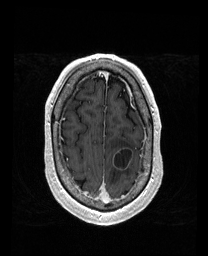
Brain MRI from a brain-tumour surgery series, one axial slice. Slice 145 of 192 in the series (ordered by position). T1-weighted post-contrast. 1 mm slice thickness. 208 × 256 image matrix, field of view 211 × 260 mm. From the clinical record (not read from this slice): histopathology: Metastatic Carcinoma from Lung Adenocarcinoma; tumour location: Left Frontal.
Outlined on this slice (outlined manually by an expert reader):
- tumour: bounding box <113,148,133,170> (left, top, right, bottom; pixels)